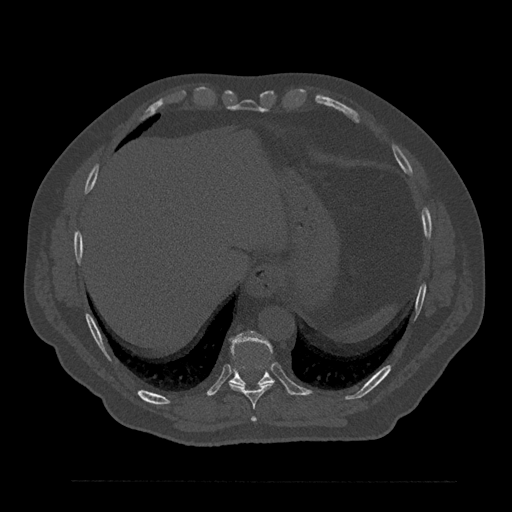
CT including the spine, one axial slice. Position 383 of 797 along the scan axis. Reconstruction kernel Br40s/3. Bone window (W 1800 / L 400 HU). 0.5 mm slice thickness. 512 × 512 image matrix, field of view 430 × 430 mm. Patient: male, 61 years. Case-level facts recorded for this patient, not image findings: primary cancer: prostate.
Structures marked on this image (semi-automatically segmented with operator editing):
- T10 vertebra: bounding box [x1, y1, x2, y2] px = [229, 331, 273, 386]
- T8 vertebra: [252, 417, 257, 422]
- T9 vertebra: [229, 366, 274, 409]